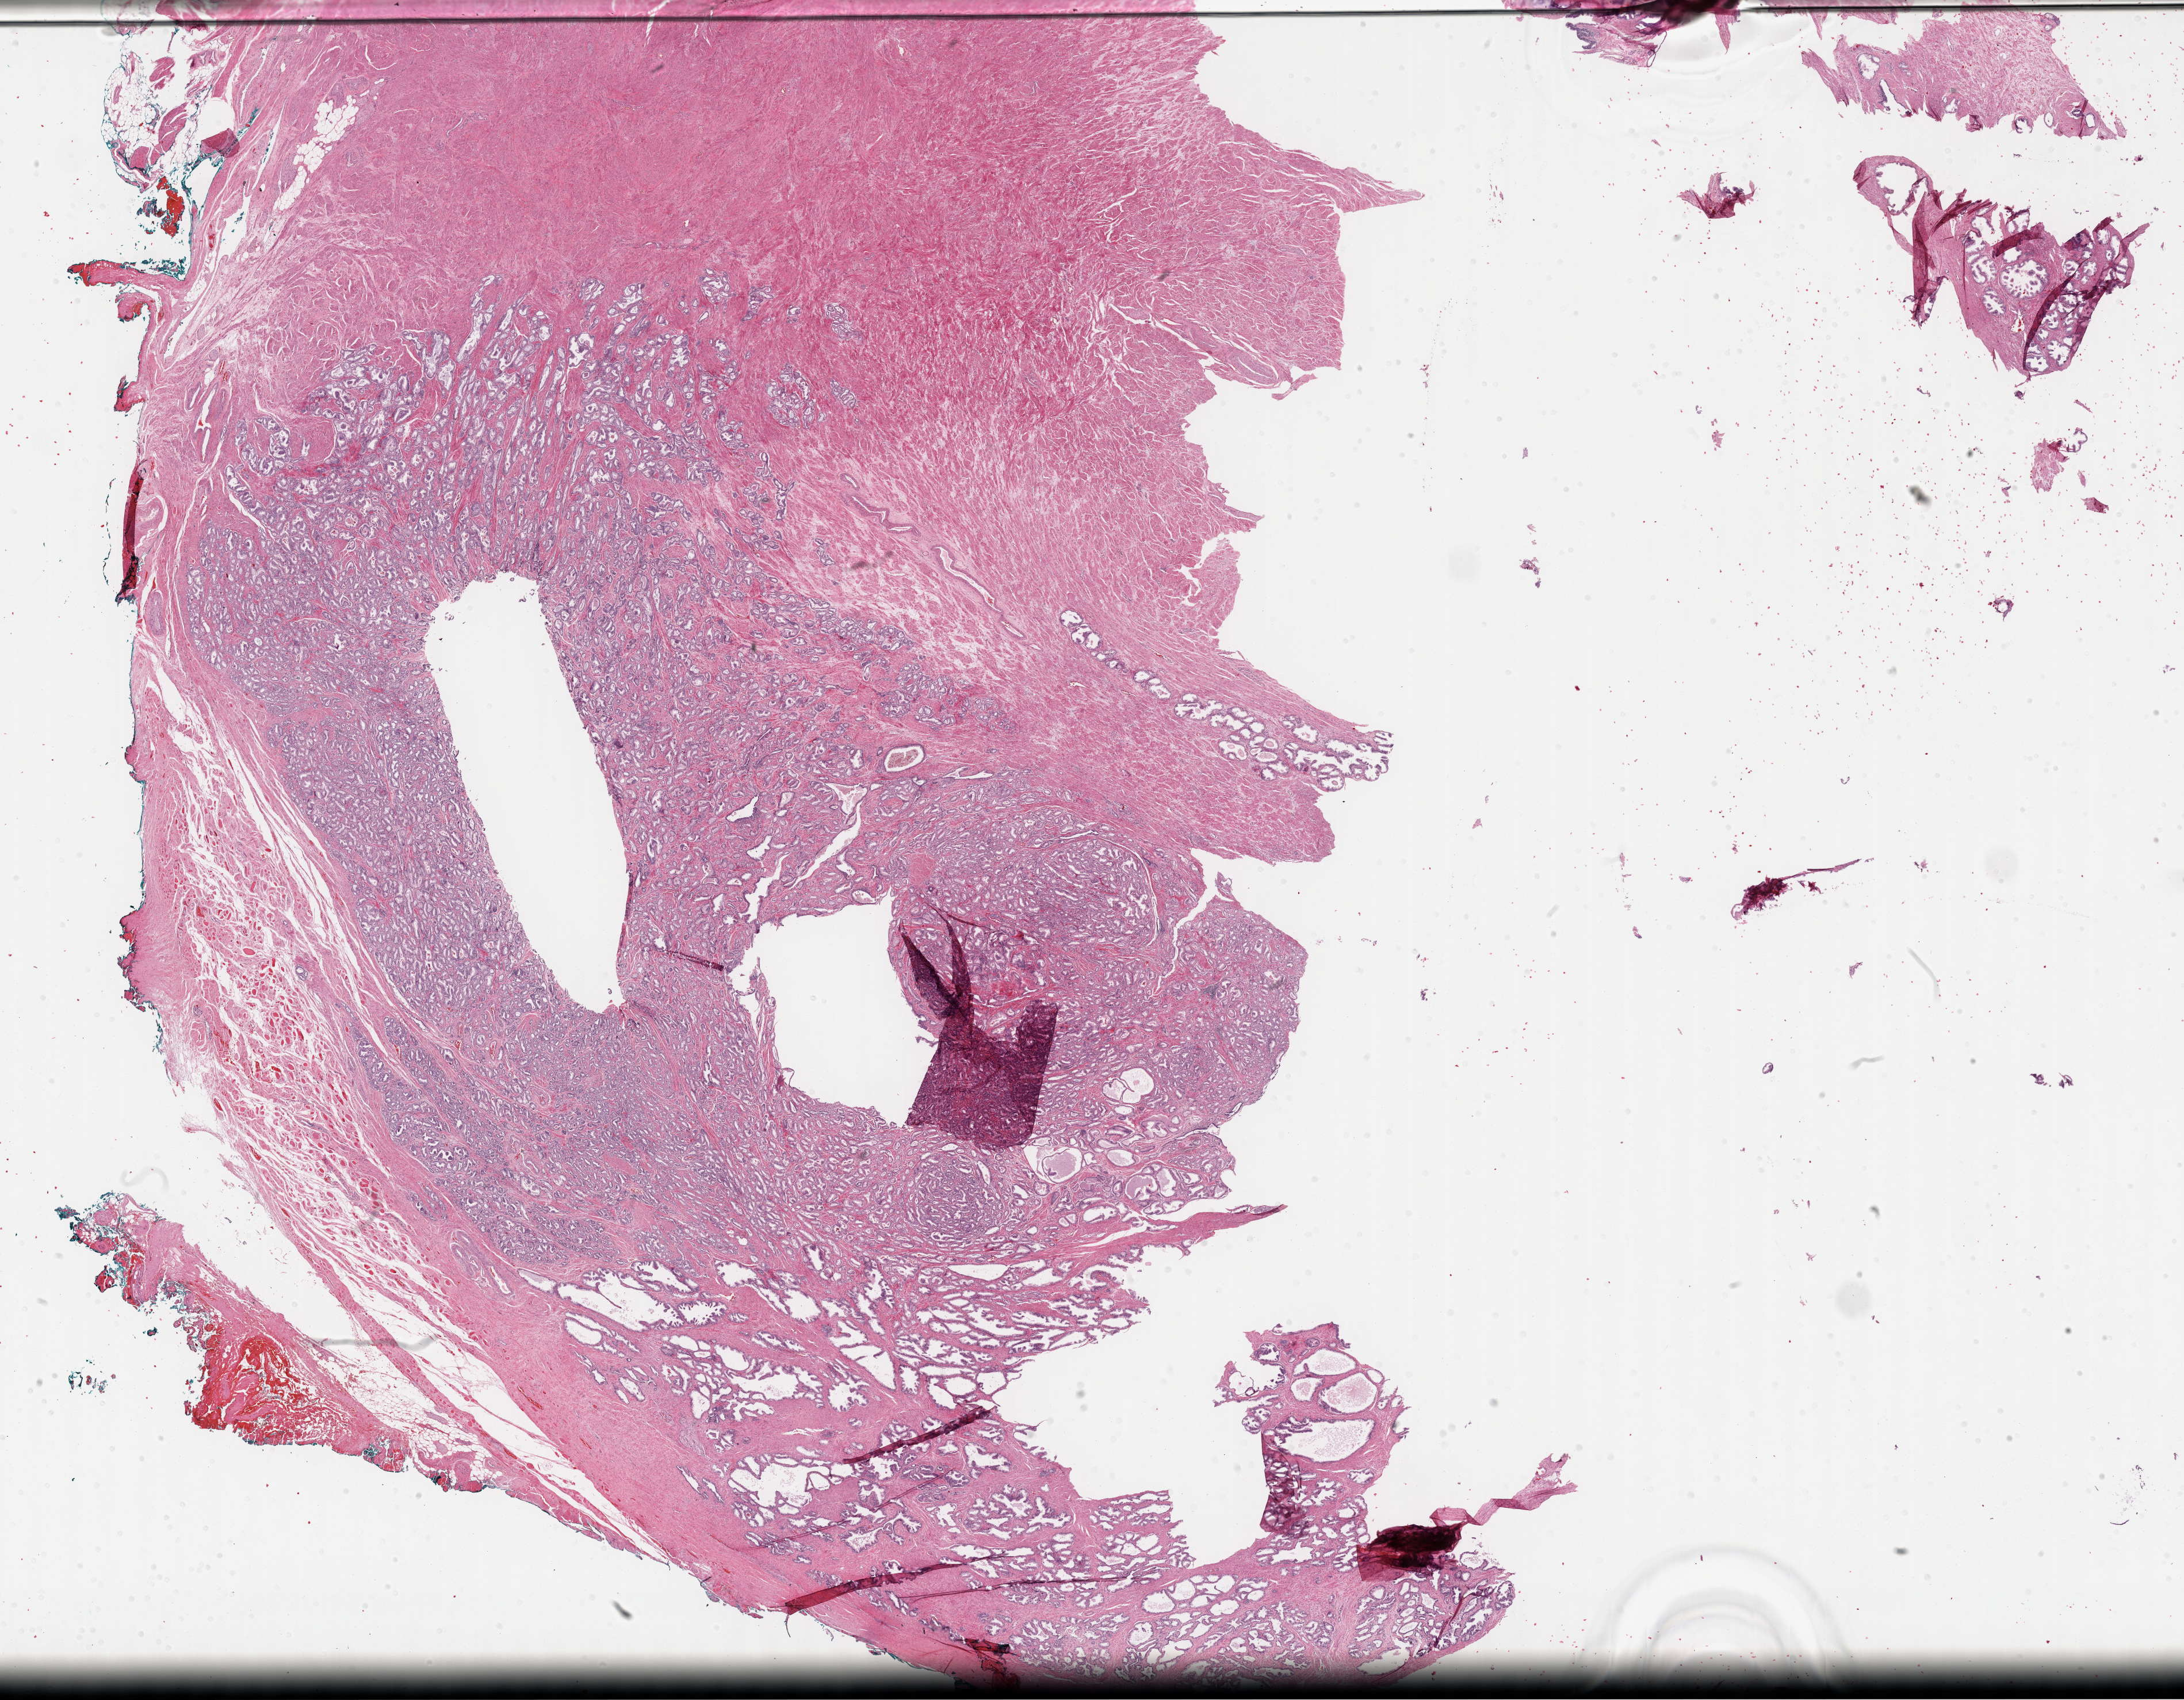
Digitized Hematoxylin and eosin (H&E) stained tissue section (whole slide), low-resolution overview of the scanned area, about 30.7 x 23.9 mm (from a 40x scan). Formalin-fixed paraffin-embedded (FFPE) diagnostic section. Sample: primary tumour, prostate. Male patient; age at initial diagnosis 57 years. Gleason score: 7 (3+4).
Diagnosis: Adenocarcinoma, NOS (prostate gland). Laterality: right.